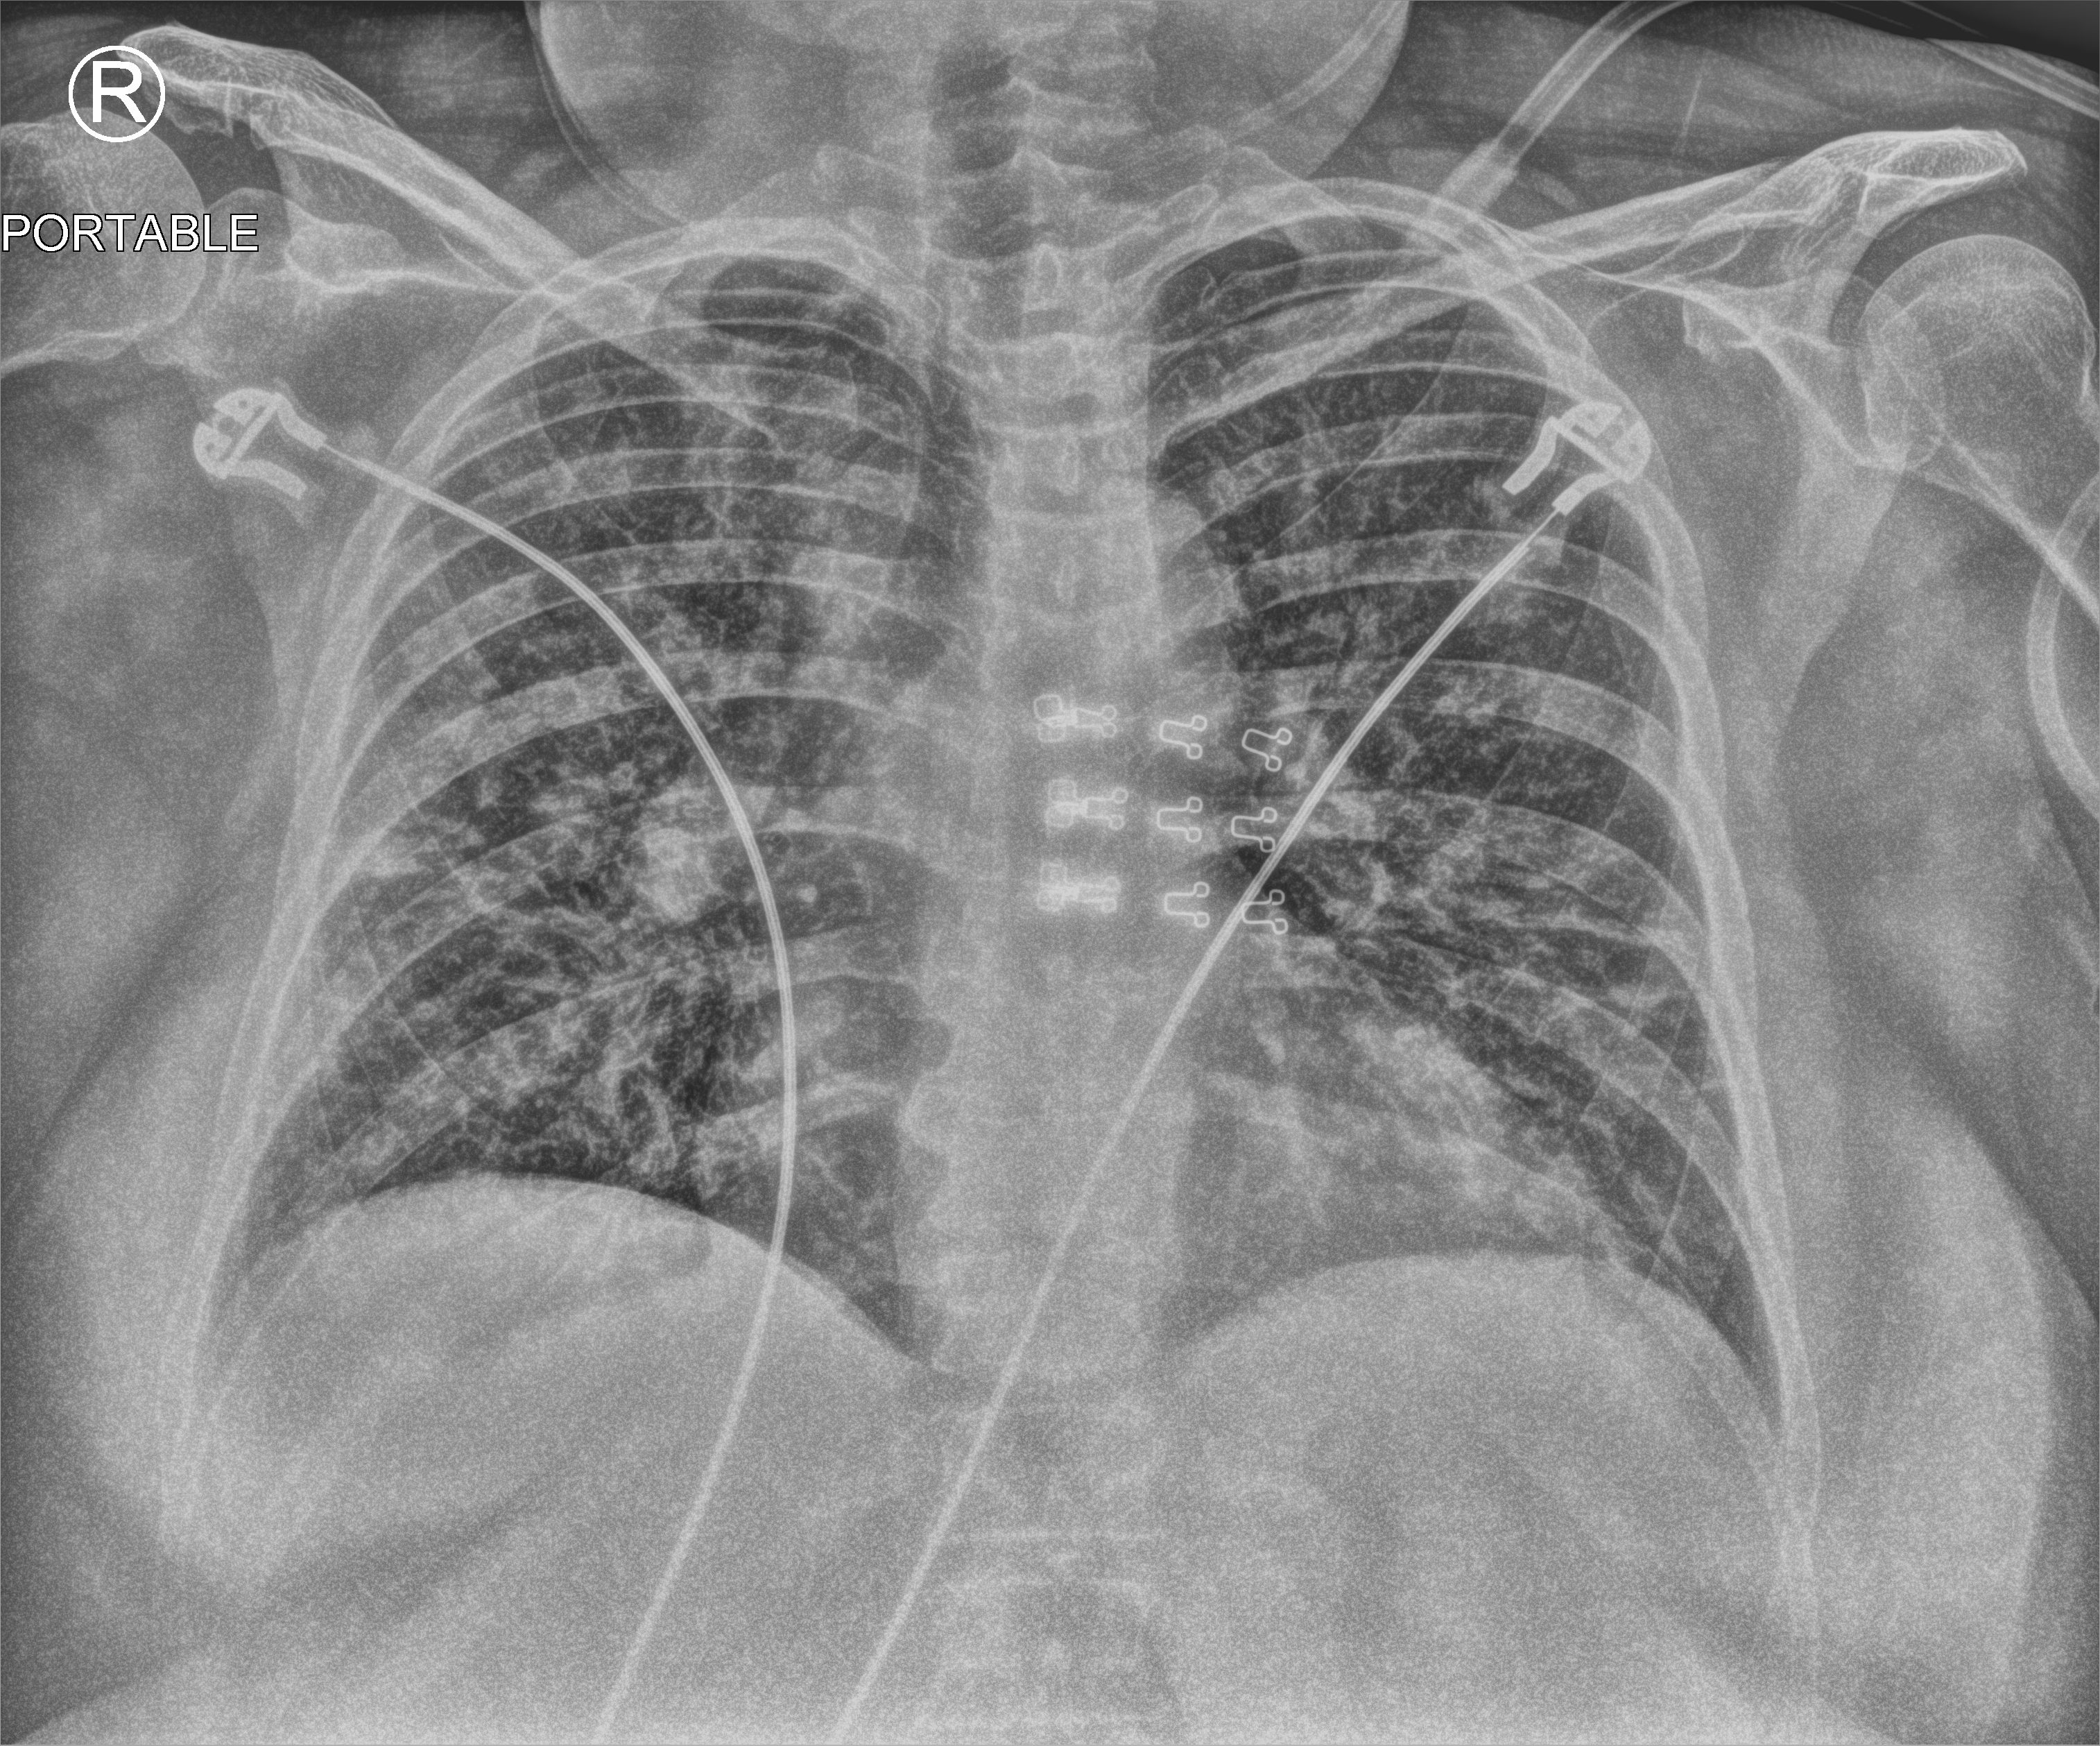
Bedside chest radiograph (computed radiography); anteroposterior (AP) projection. Patient hospitalised with COVID-19; female, aged 18–59 years.
Admission-level facts for this patient (not findings on this image; timing relative to this image not recorded):
- admitted to intensive care during this hospital stay: no
- hypertension (admission record): yes